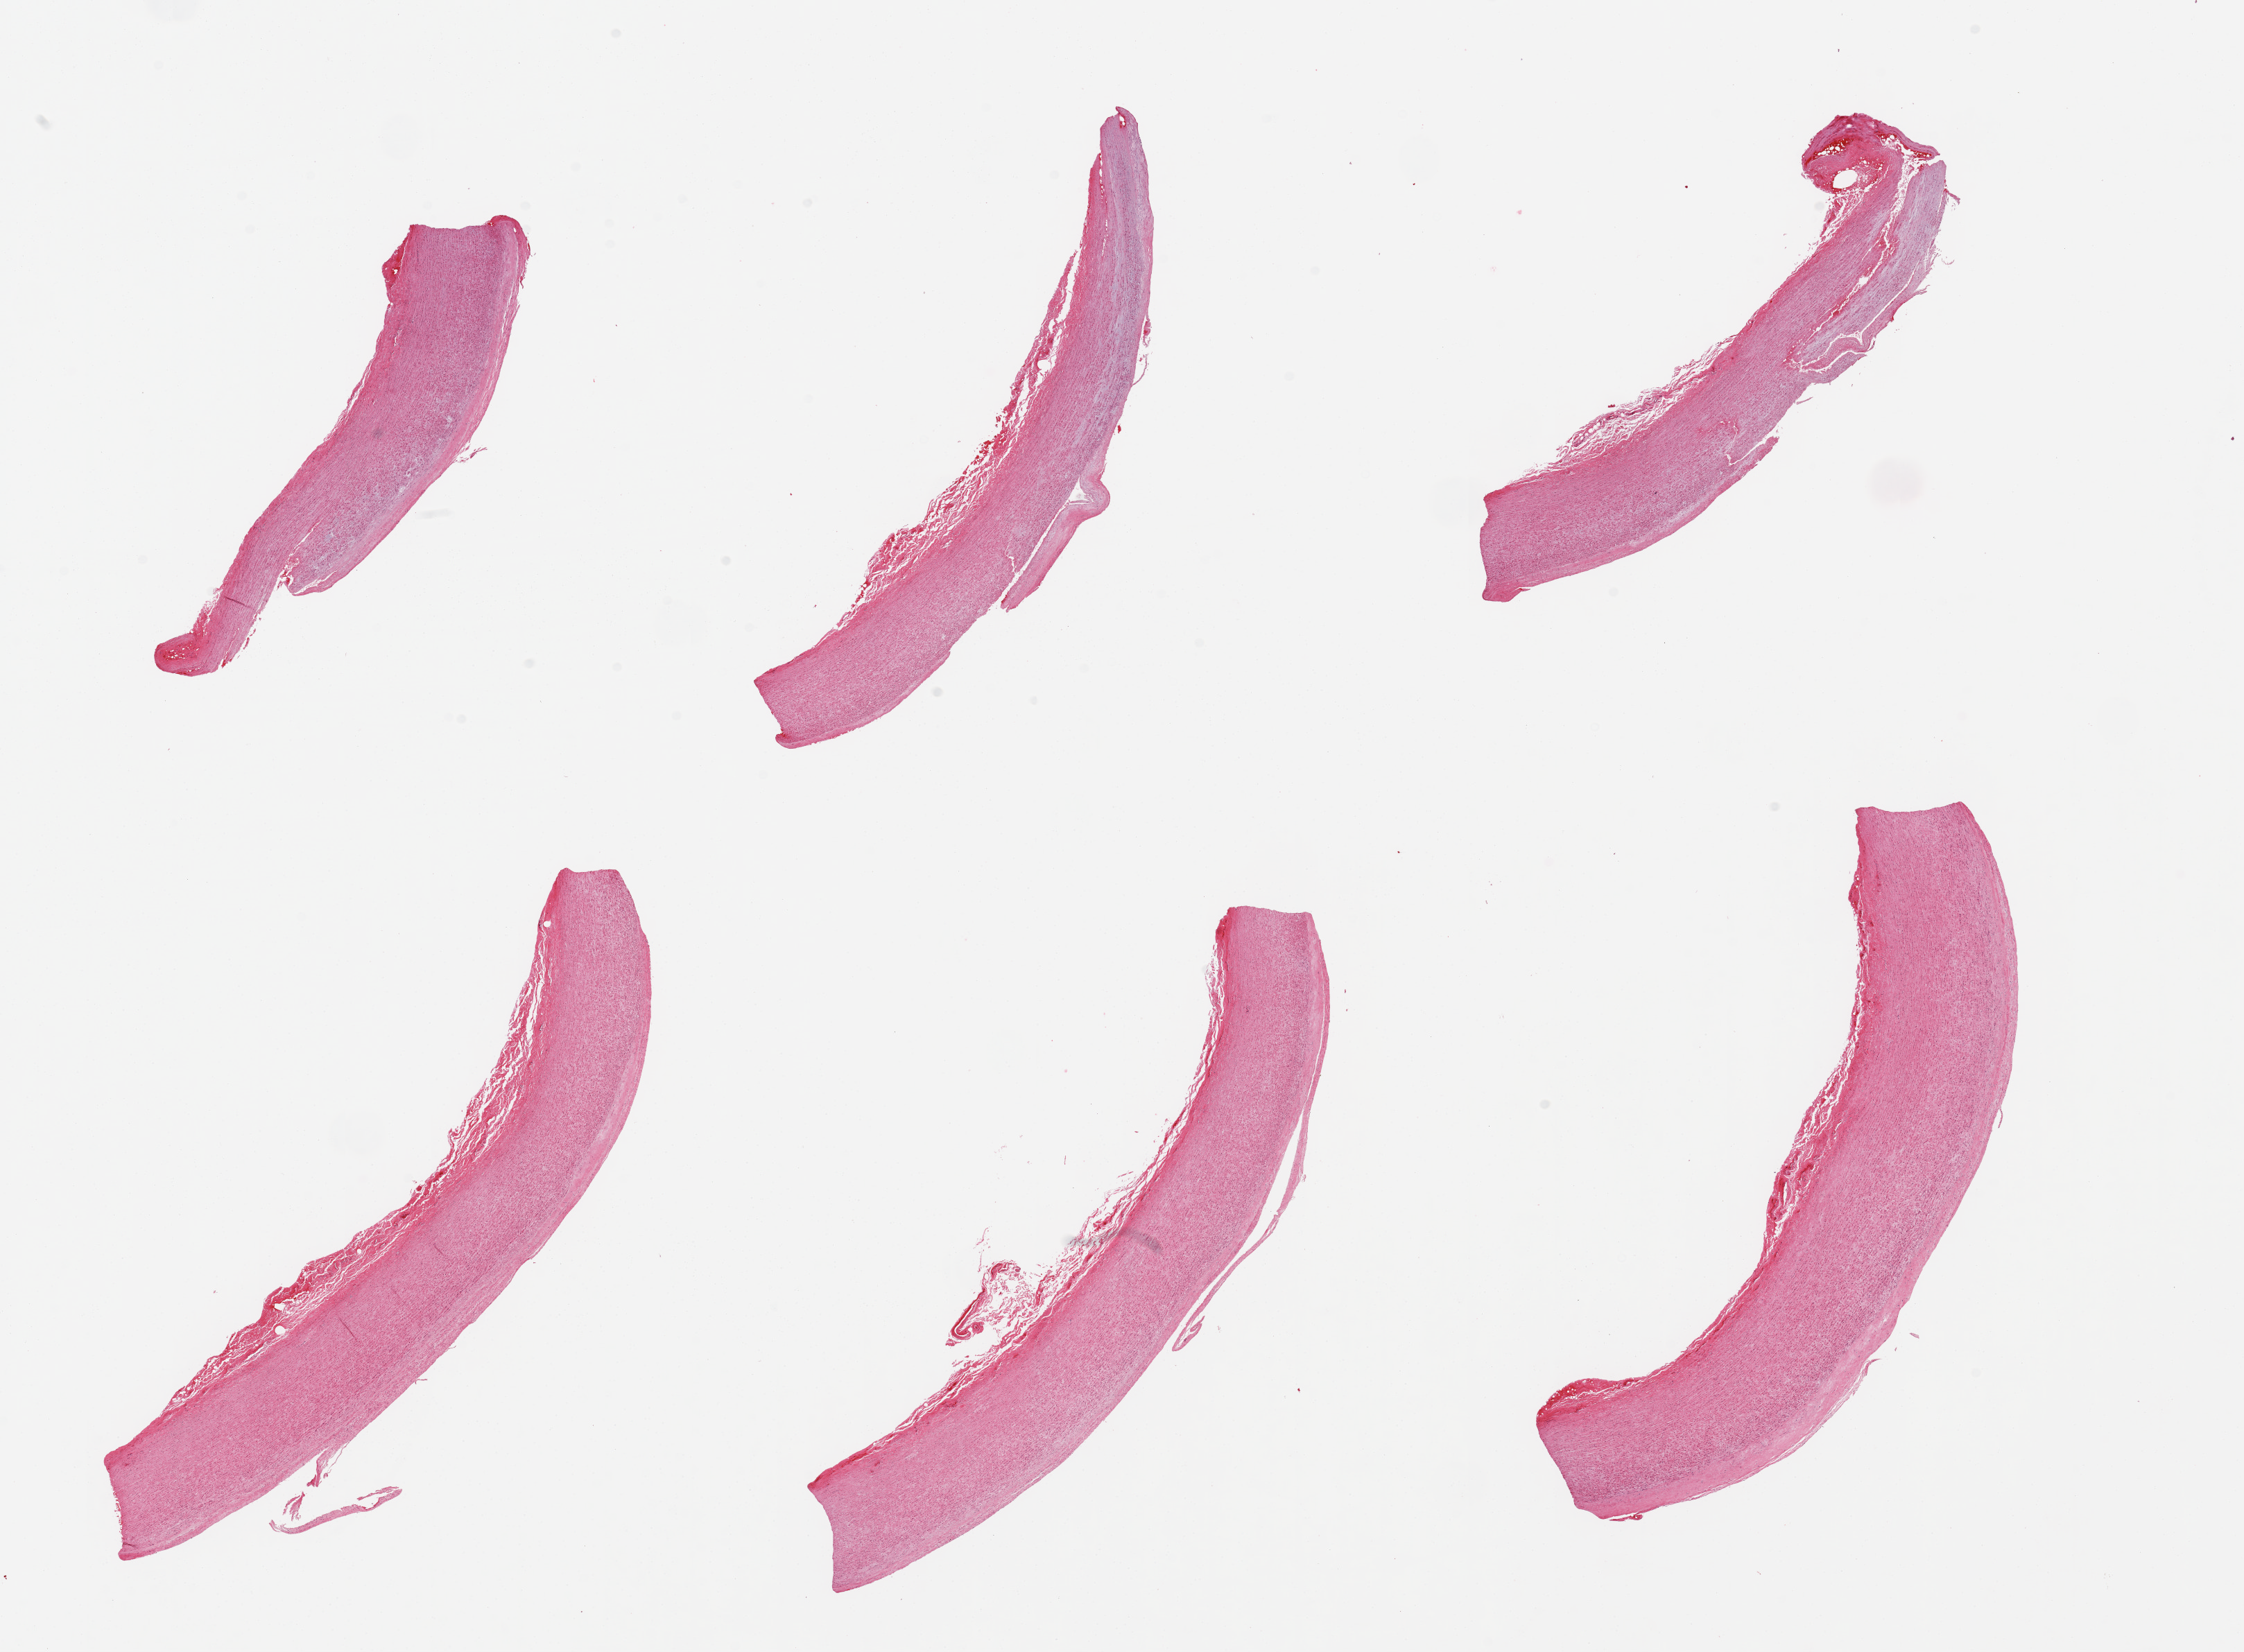
Hematoxylin and eosin (H&E) whole-slide image — shown as a low-resolution overview of the whole scanned area (about 25.6 x 18.8 mm, acquisition: 20x scan); PAXgene-fixed paraffin-embedded (PFPE) section; sampled site (target tissue): aorta; tissue donor sample.
Pathologist's review note for this sample: 6 pieces; atherosclerotic plaque.